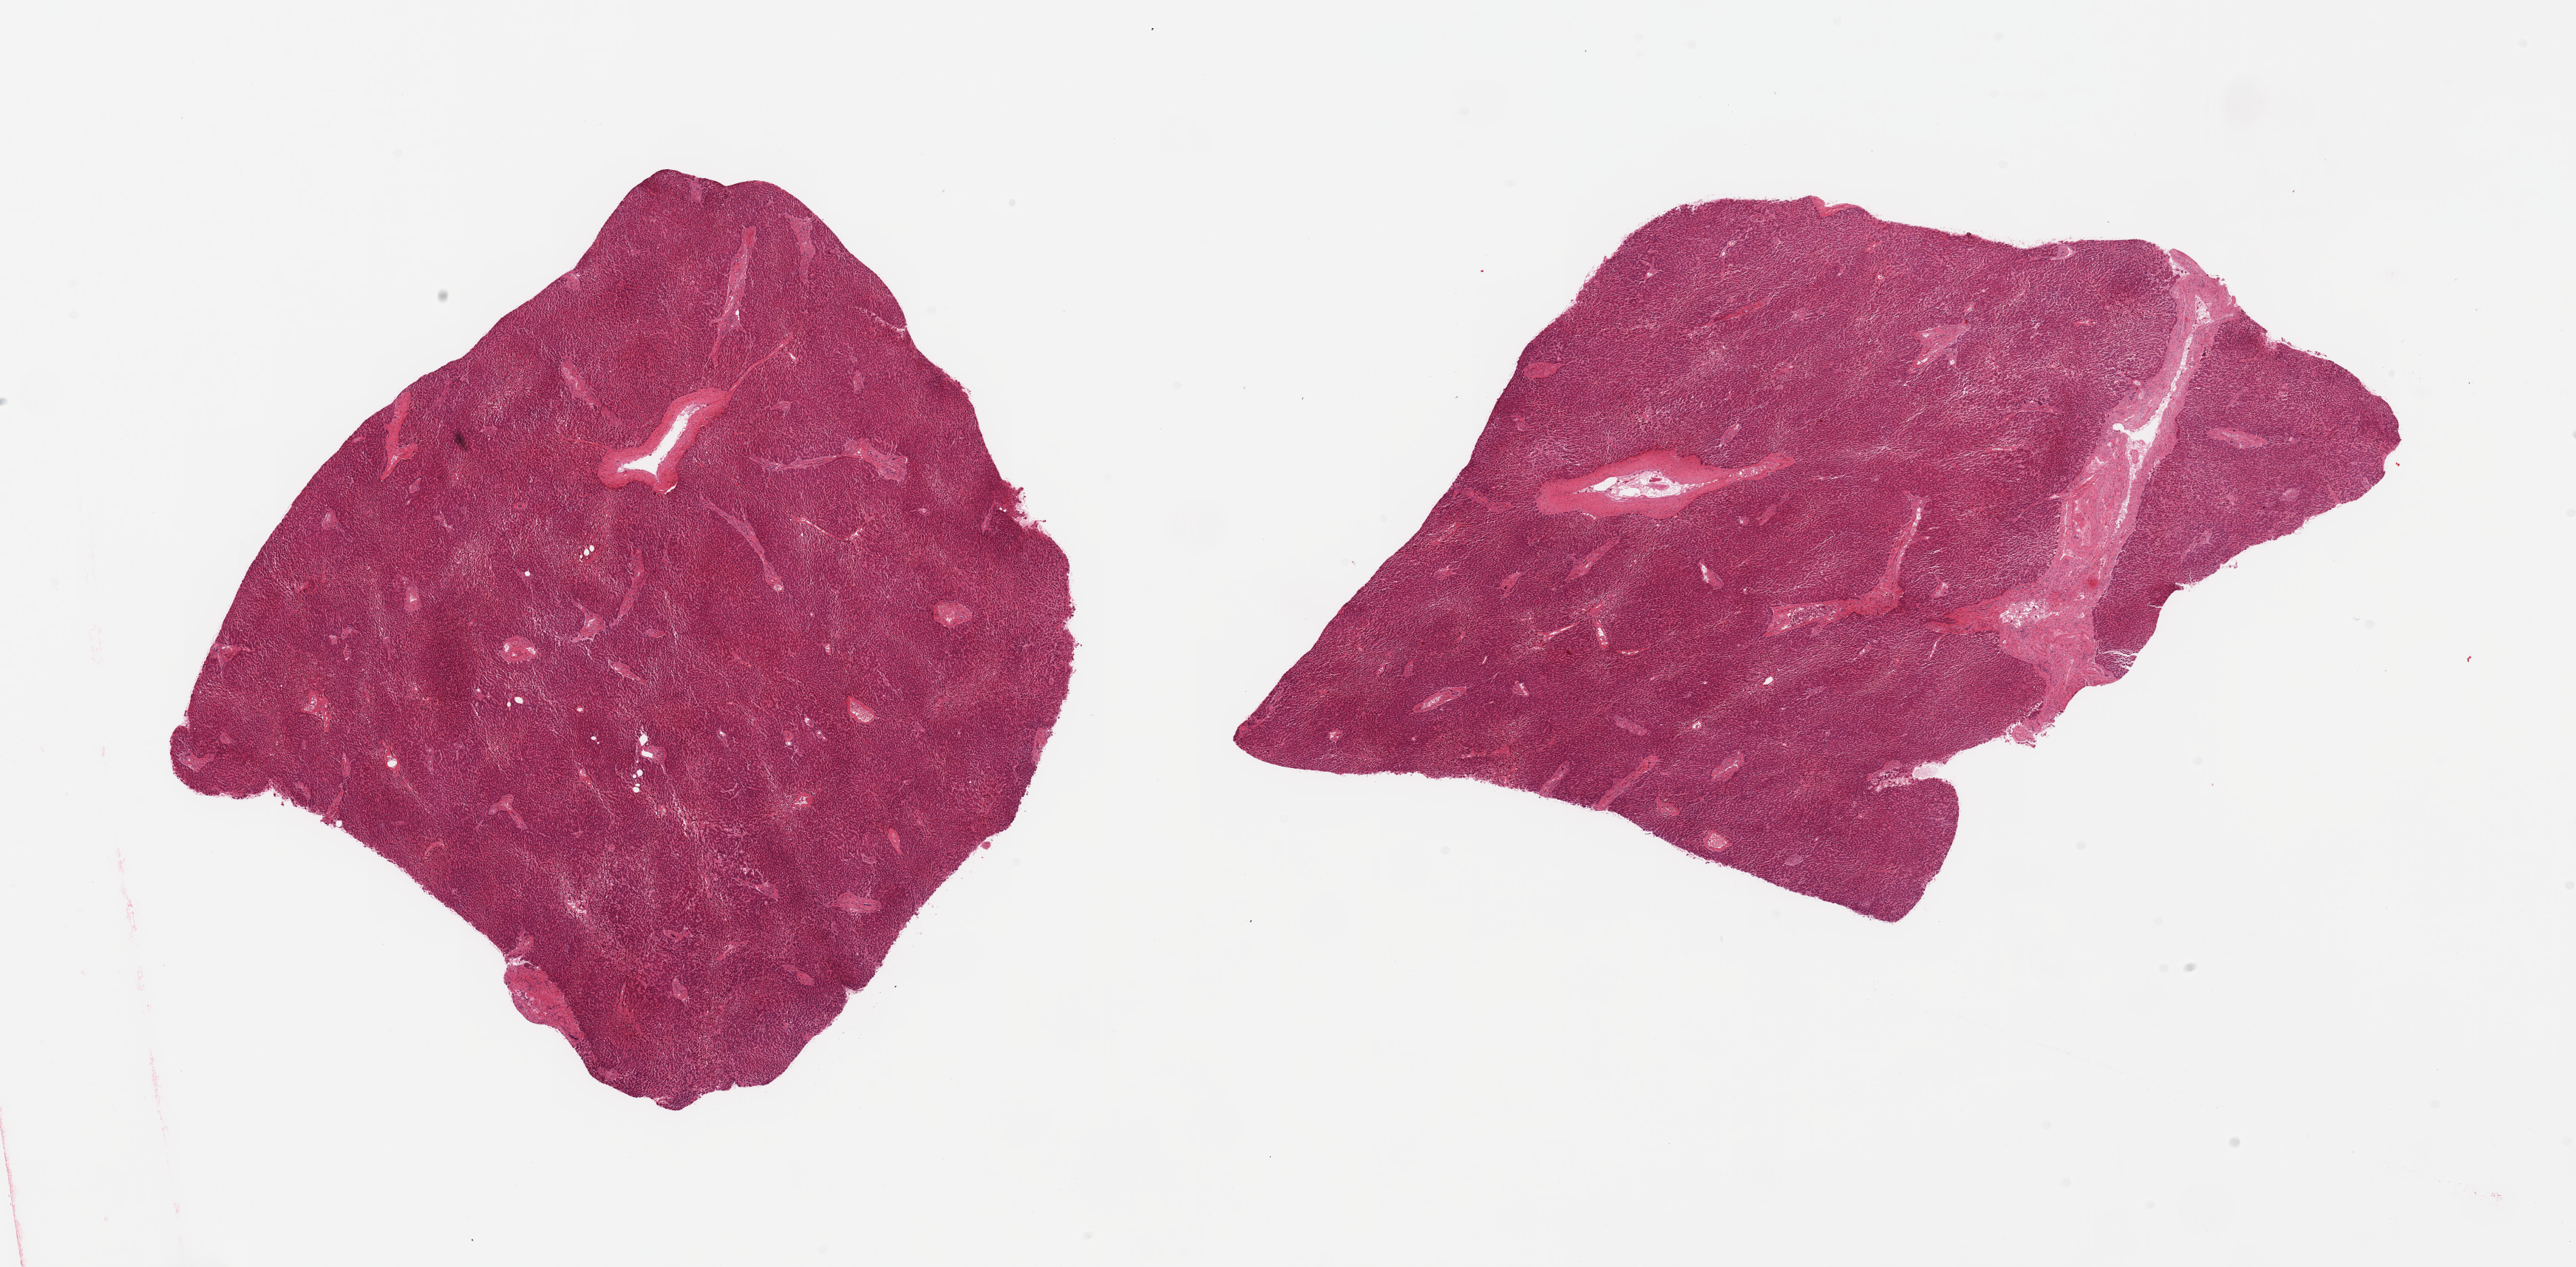
Haematoxylin and eosin whole-slide image, shown as a low-resolution overview of the whole scanned area (about 27.6 x 13.6 mm), PAXgene-fixed paraffin-embedded (PFPE) section, section of liver (target tissue), tissue donor sample. Donor sex: female.
* reviewer comment on this tissue sample: 2 pieces; focal macrovesicular steatosis <5%